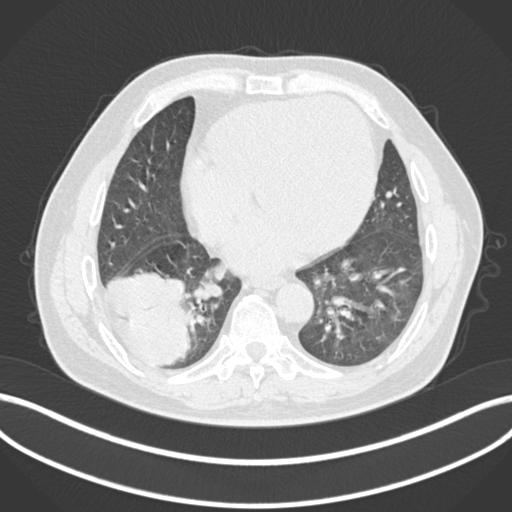
Chest CT, one axial slice; position 52 of 200 along the scan axis; reconstruction kernel B30f; 120 kVp; lung window (W 1500 / L -600 HU); 1 mm slice thickness; 512 × 512 image matrix, field of view 400 × 400 mm. Patient: male, 59 years.
Structures marked on this image (bounding box drawn by a radiologist):
- lung tumour (recorded histology: adenocarcinoma): bounding box [x1, y1, x2, y2] px = [100, 268, 198, 368]